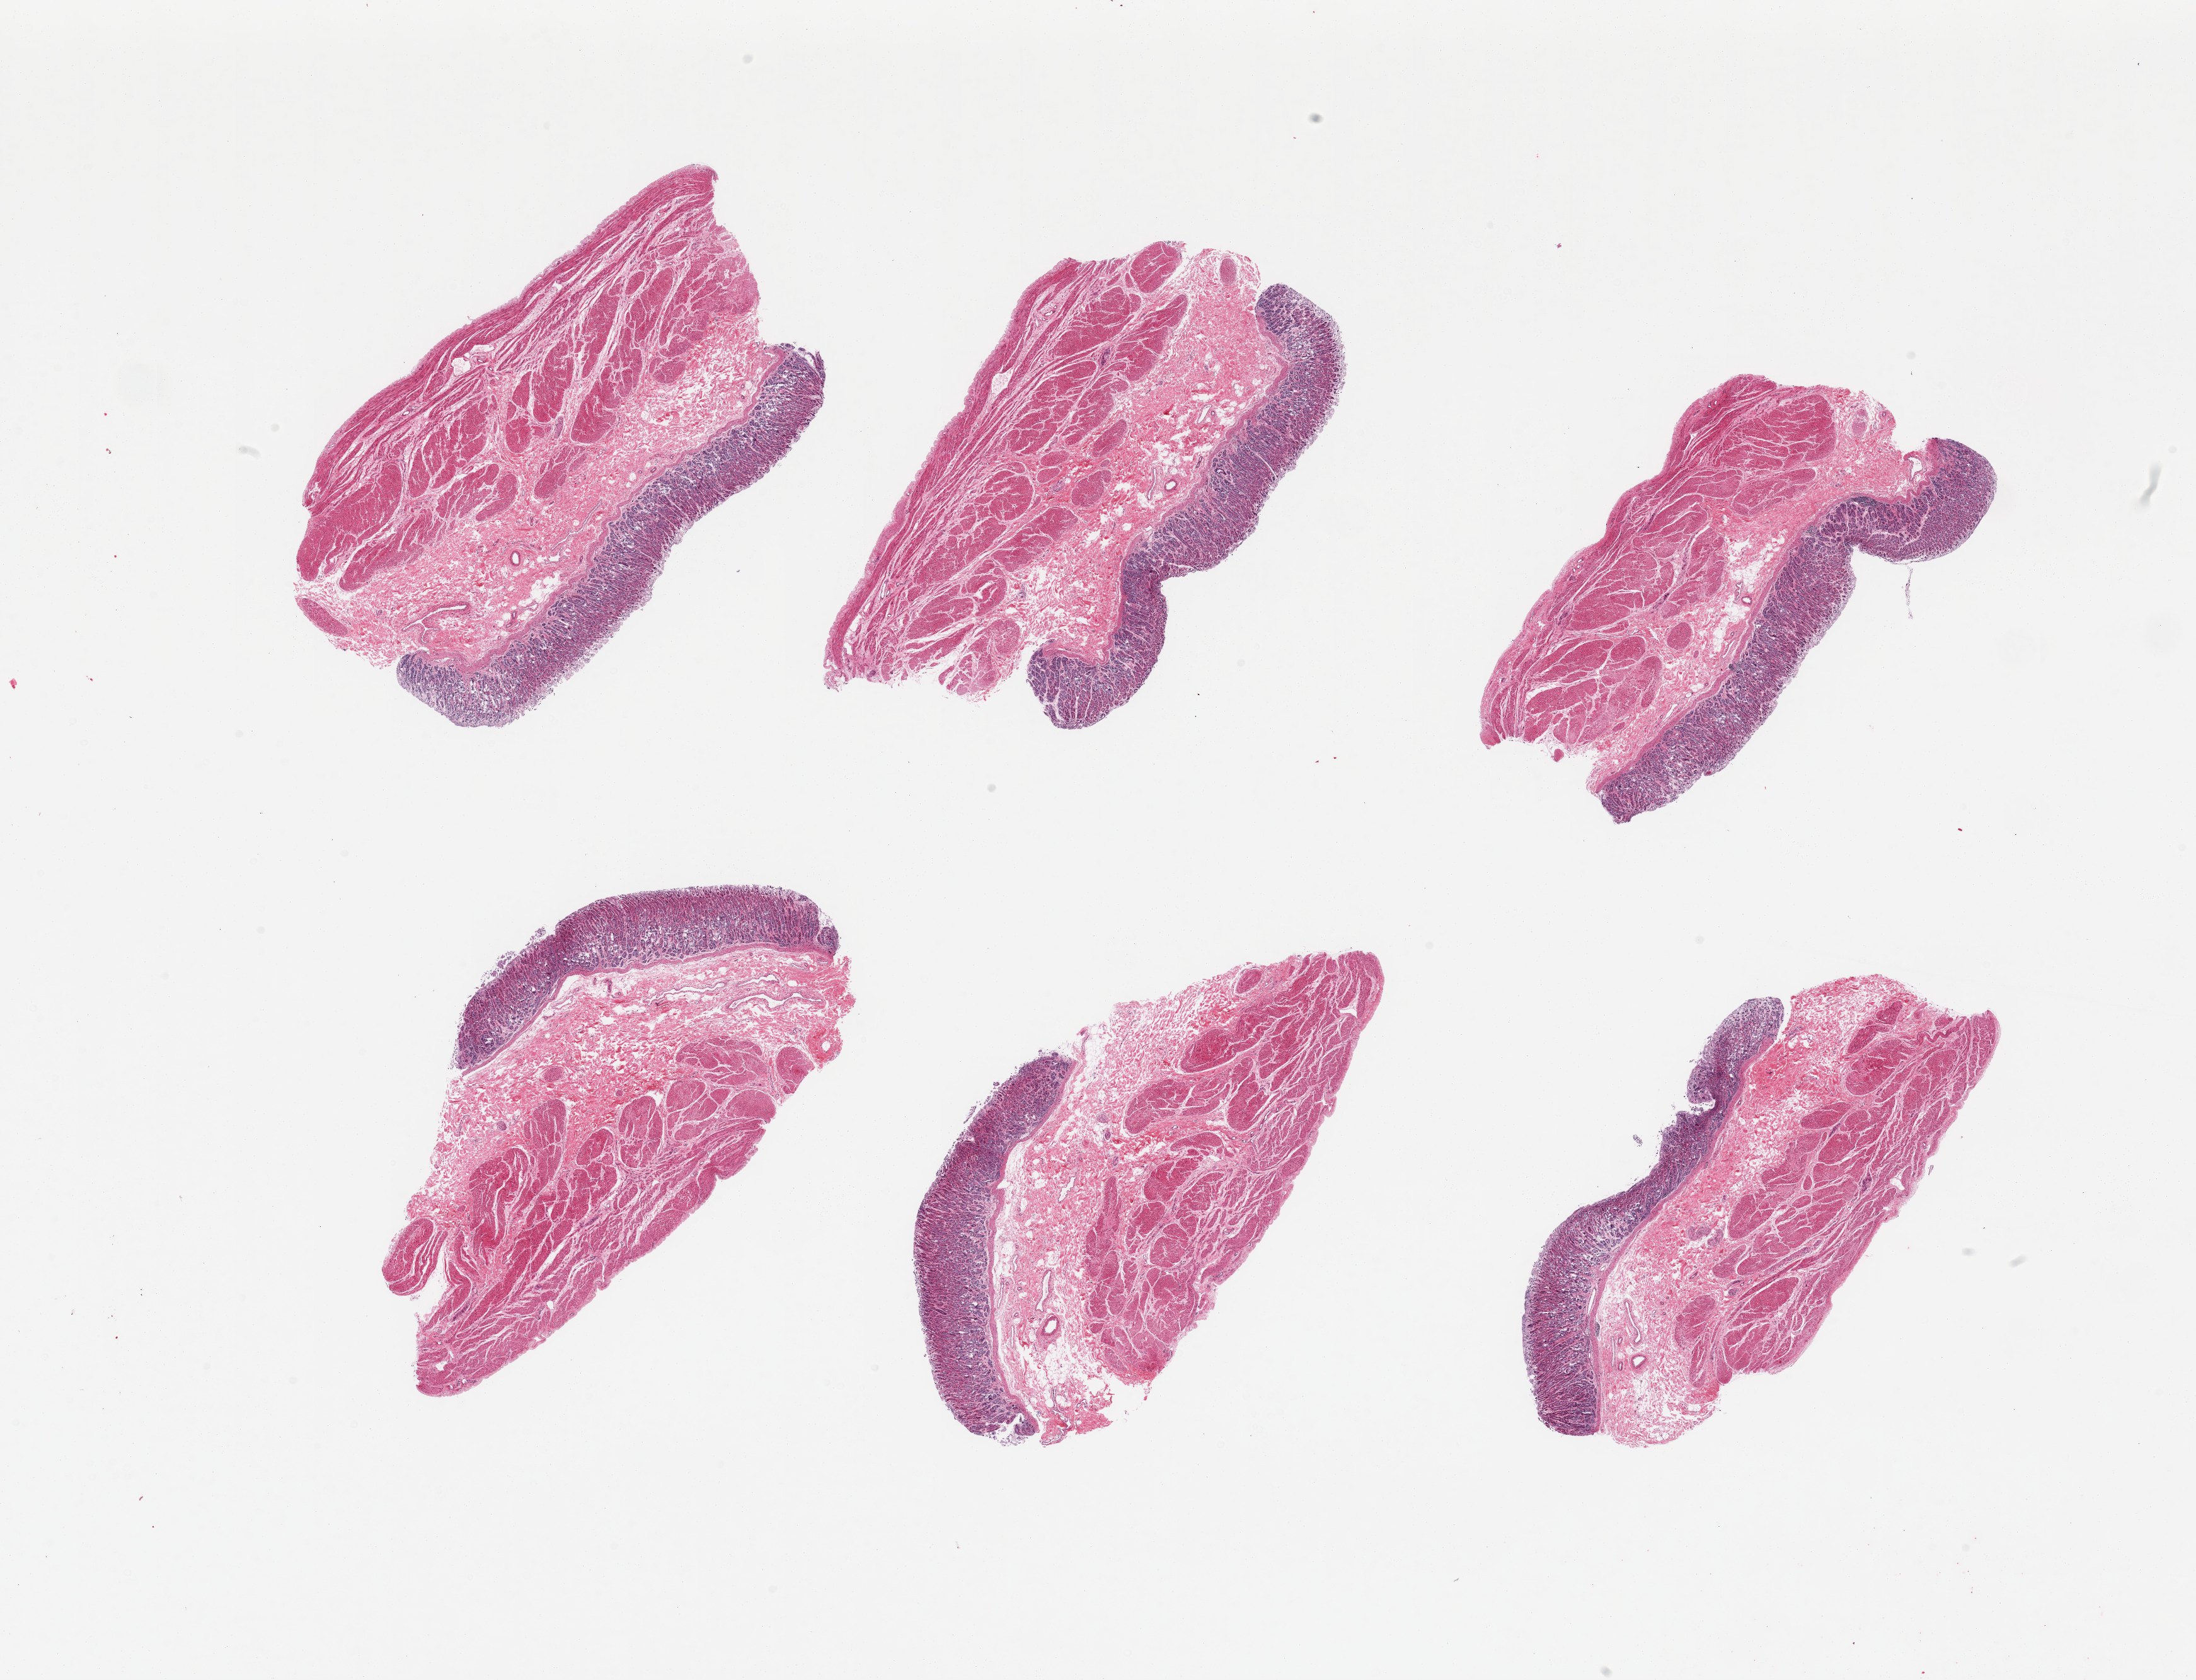
Hematoxylin and eosin (H&E) whole-slide image, brightfield — whole scanned area (about 27.6 x 21.1 mm, acquisition: 20x scan) shown as a low-resolution overview. PAXgene-fixed paraffin-embedded (PFPE) section. Section of stomach (target tissue). Donor tissue sample. Male donor.
Reviewer comment on this tissue sample: 6 pieces; mild to focally moderate colonic mucosa autolysis and well preserved muscularis; lymphoid aggregates.